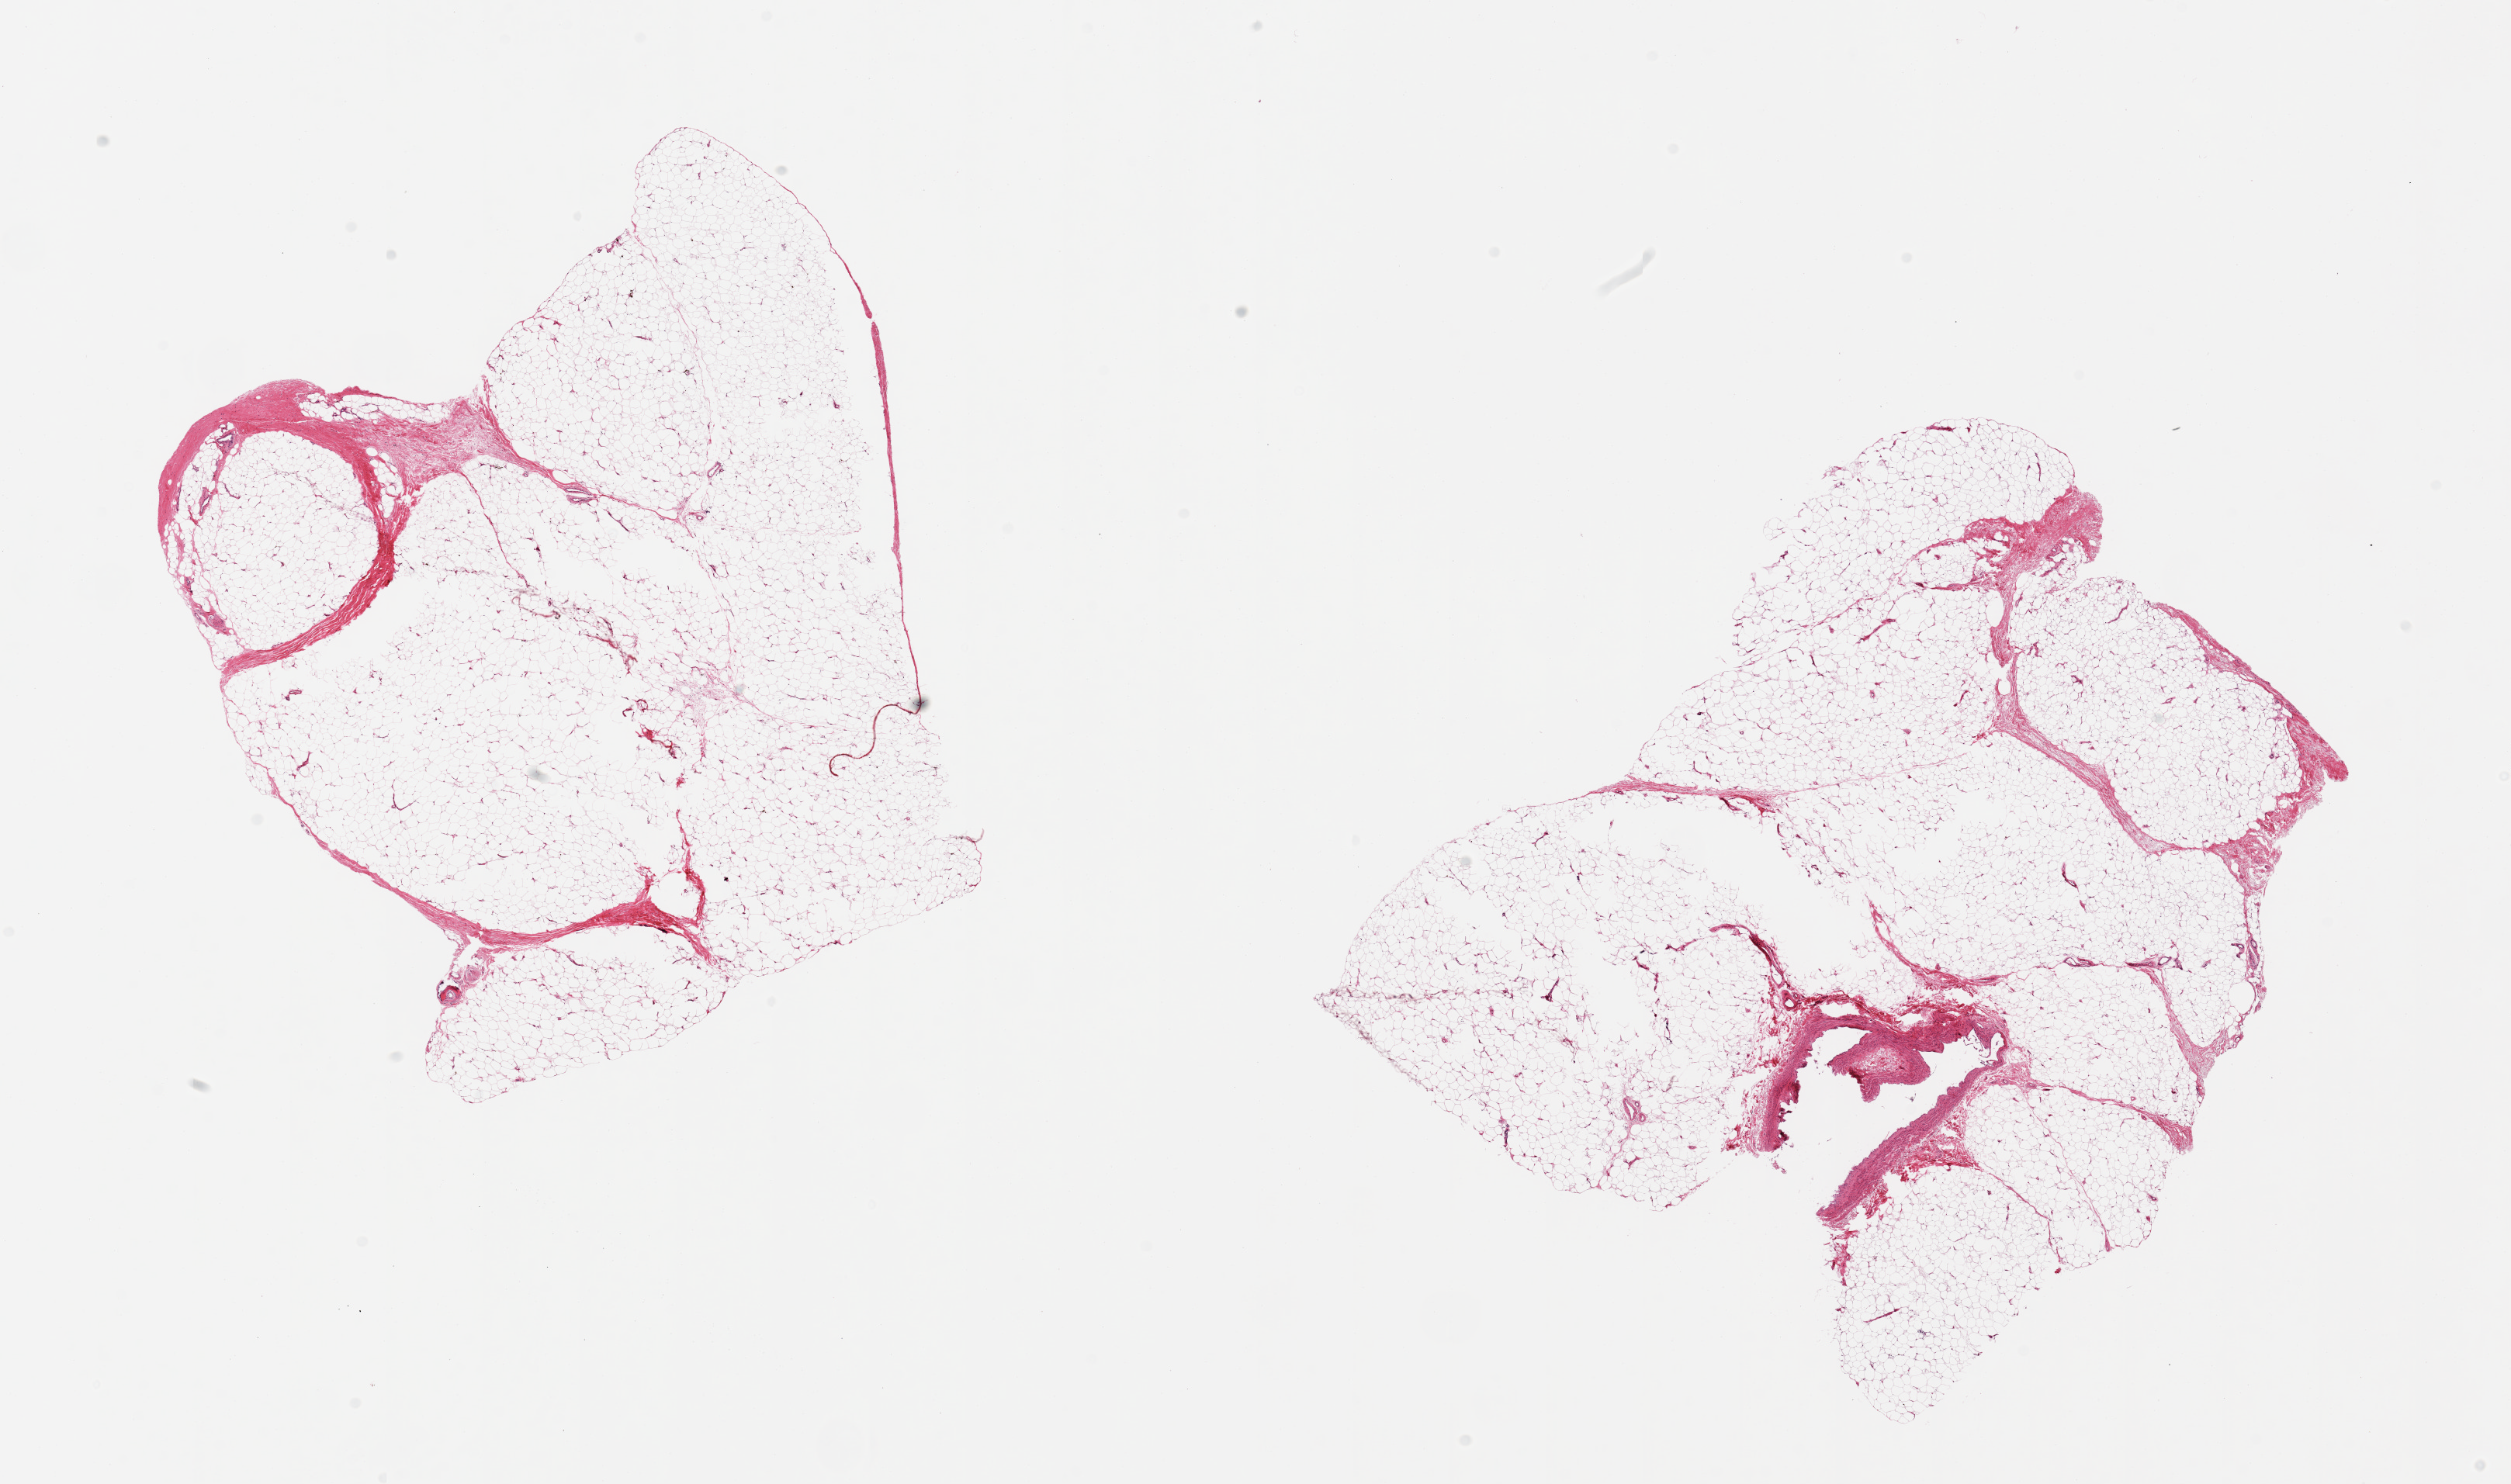
Hematoxylin and eosin (H&E) whole-slide image — low-resolution overview of the scanned area, about 25.6 x 15.1 mm, PAXgene-fixed, paraffin-embedded tissue, sampled site (target tissue): adipose tissue, donor tissue sample. Donor: male.
Reviewer comment on this tissue sample: 2 pieces; one piece includes large vessel.